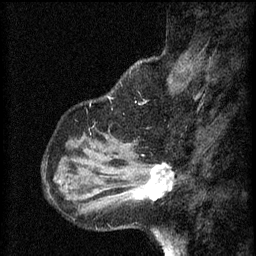
Breast MRI (dynamic contrast-enhanced), one sagittal slice; slice 15 of 60 in the series (ordered by position); 3 images stored at this slice position (order not interpretable as contrast timing); 1.5 T; TE 4.2 ms, TR 8.2 ms; 256 × 256 image matrix, field of view 180 × 180 mm. Patient: female, 37 years.
Annotated regions visible in this slice (semi-automatically segmented with operator editing):
- analysis volume of interest (the breast-tissue region the enhancement analysis was run in; not a lesion): bounding box <126,156,175,205> (left, top, right, bottom; pixels)
- tumour enhancement mask (voxels above the 70 % enhancement threshold inside the analysis volume of interest): <134,164,174,201>